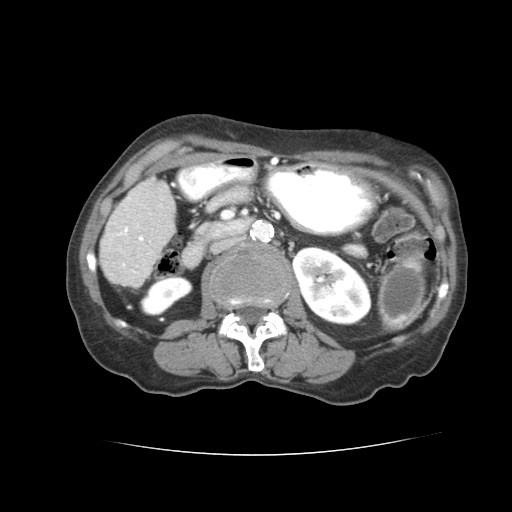
Contrast-enhanced abdominal CT (liver protocol), one axial slice. Slice 18 of 77 in the series (ordered by position). Reconstruction kernel STANDARD. Soft-tissue window (W 400 / L 40 HU). 512 × 512 image matrix. From the clinical record (not read from this slice): diagnosis: hepatocellular carcinoma (patient treated with transarterial chemoembolisation; whether this scan precedes or follows treatment is not stated here); TNM stage (as recorded): Stage-I; Child-Pugh class: A; tumour differentiation: well differentiated; tumour size: 7.6 cm.
Outlined on this slice (semi-automatic segmentation, software-assisted and operator-edited):
- liver parenchyma outside the tumour (the mass and vessels are separate outlines, so this box may not span the whole liver): bounding box [x1, y1, x2, y2] px = [100, 178, 172, 284]
- liver vessels: [121, 226, 150, 263]